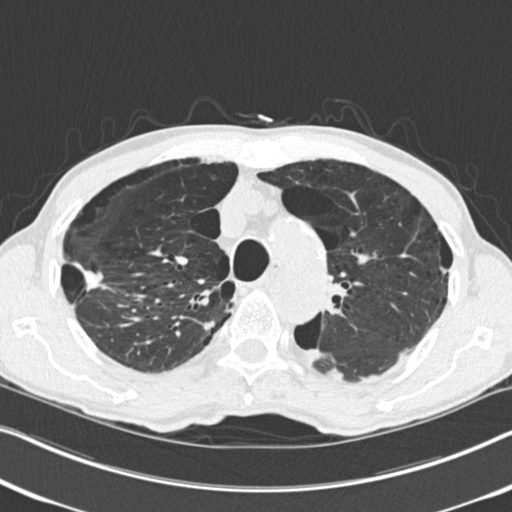
Low-dose screening chest CT, axial slice; second annual screen; lung window (W 1500 / L -600 HU); 2 mm slice thickness; 512 × 512 image matrix. Male participant, aged 71 years at enrolment.
Expert-annotated lung lesion, bounding box <58,240,129,316> (left, top, right, bottom; pixels). The screening reader recorded 4 non-calcified nodules or masses ≥4 mm on this exam (right upper lobe, right upper lobe, right upper lobe, left upper lobe); which of them this box marks is not recorded. Participant outcome: lung cancer diagnosed 83 days after this screen — adenocarcinoma, NOS, right upper lobe, well differentiated (G1), stage IA (AJCC 6th edition), 30 mm at pathology.